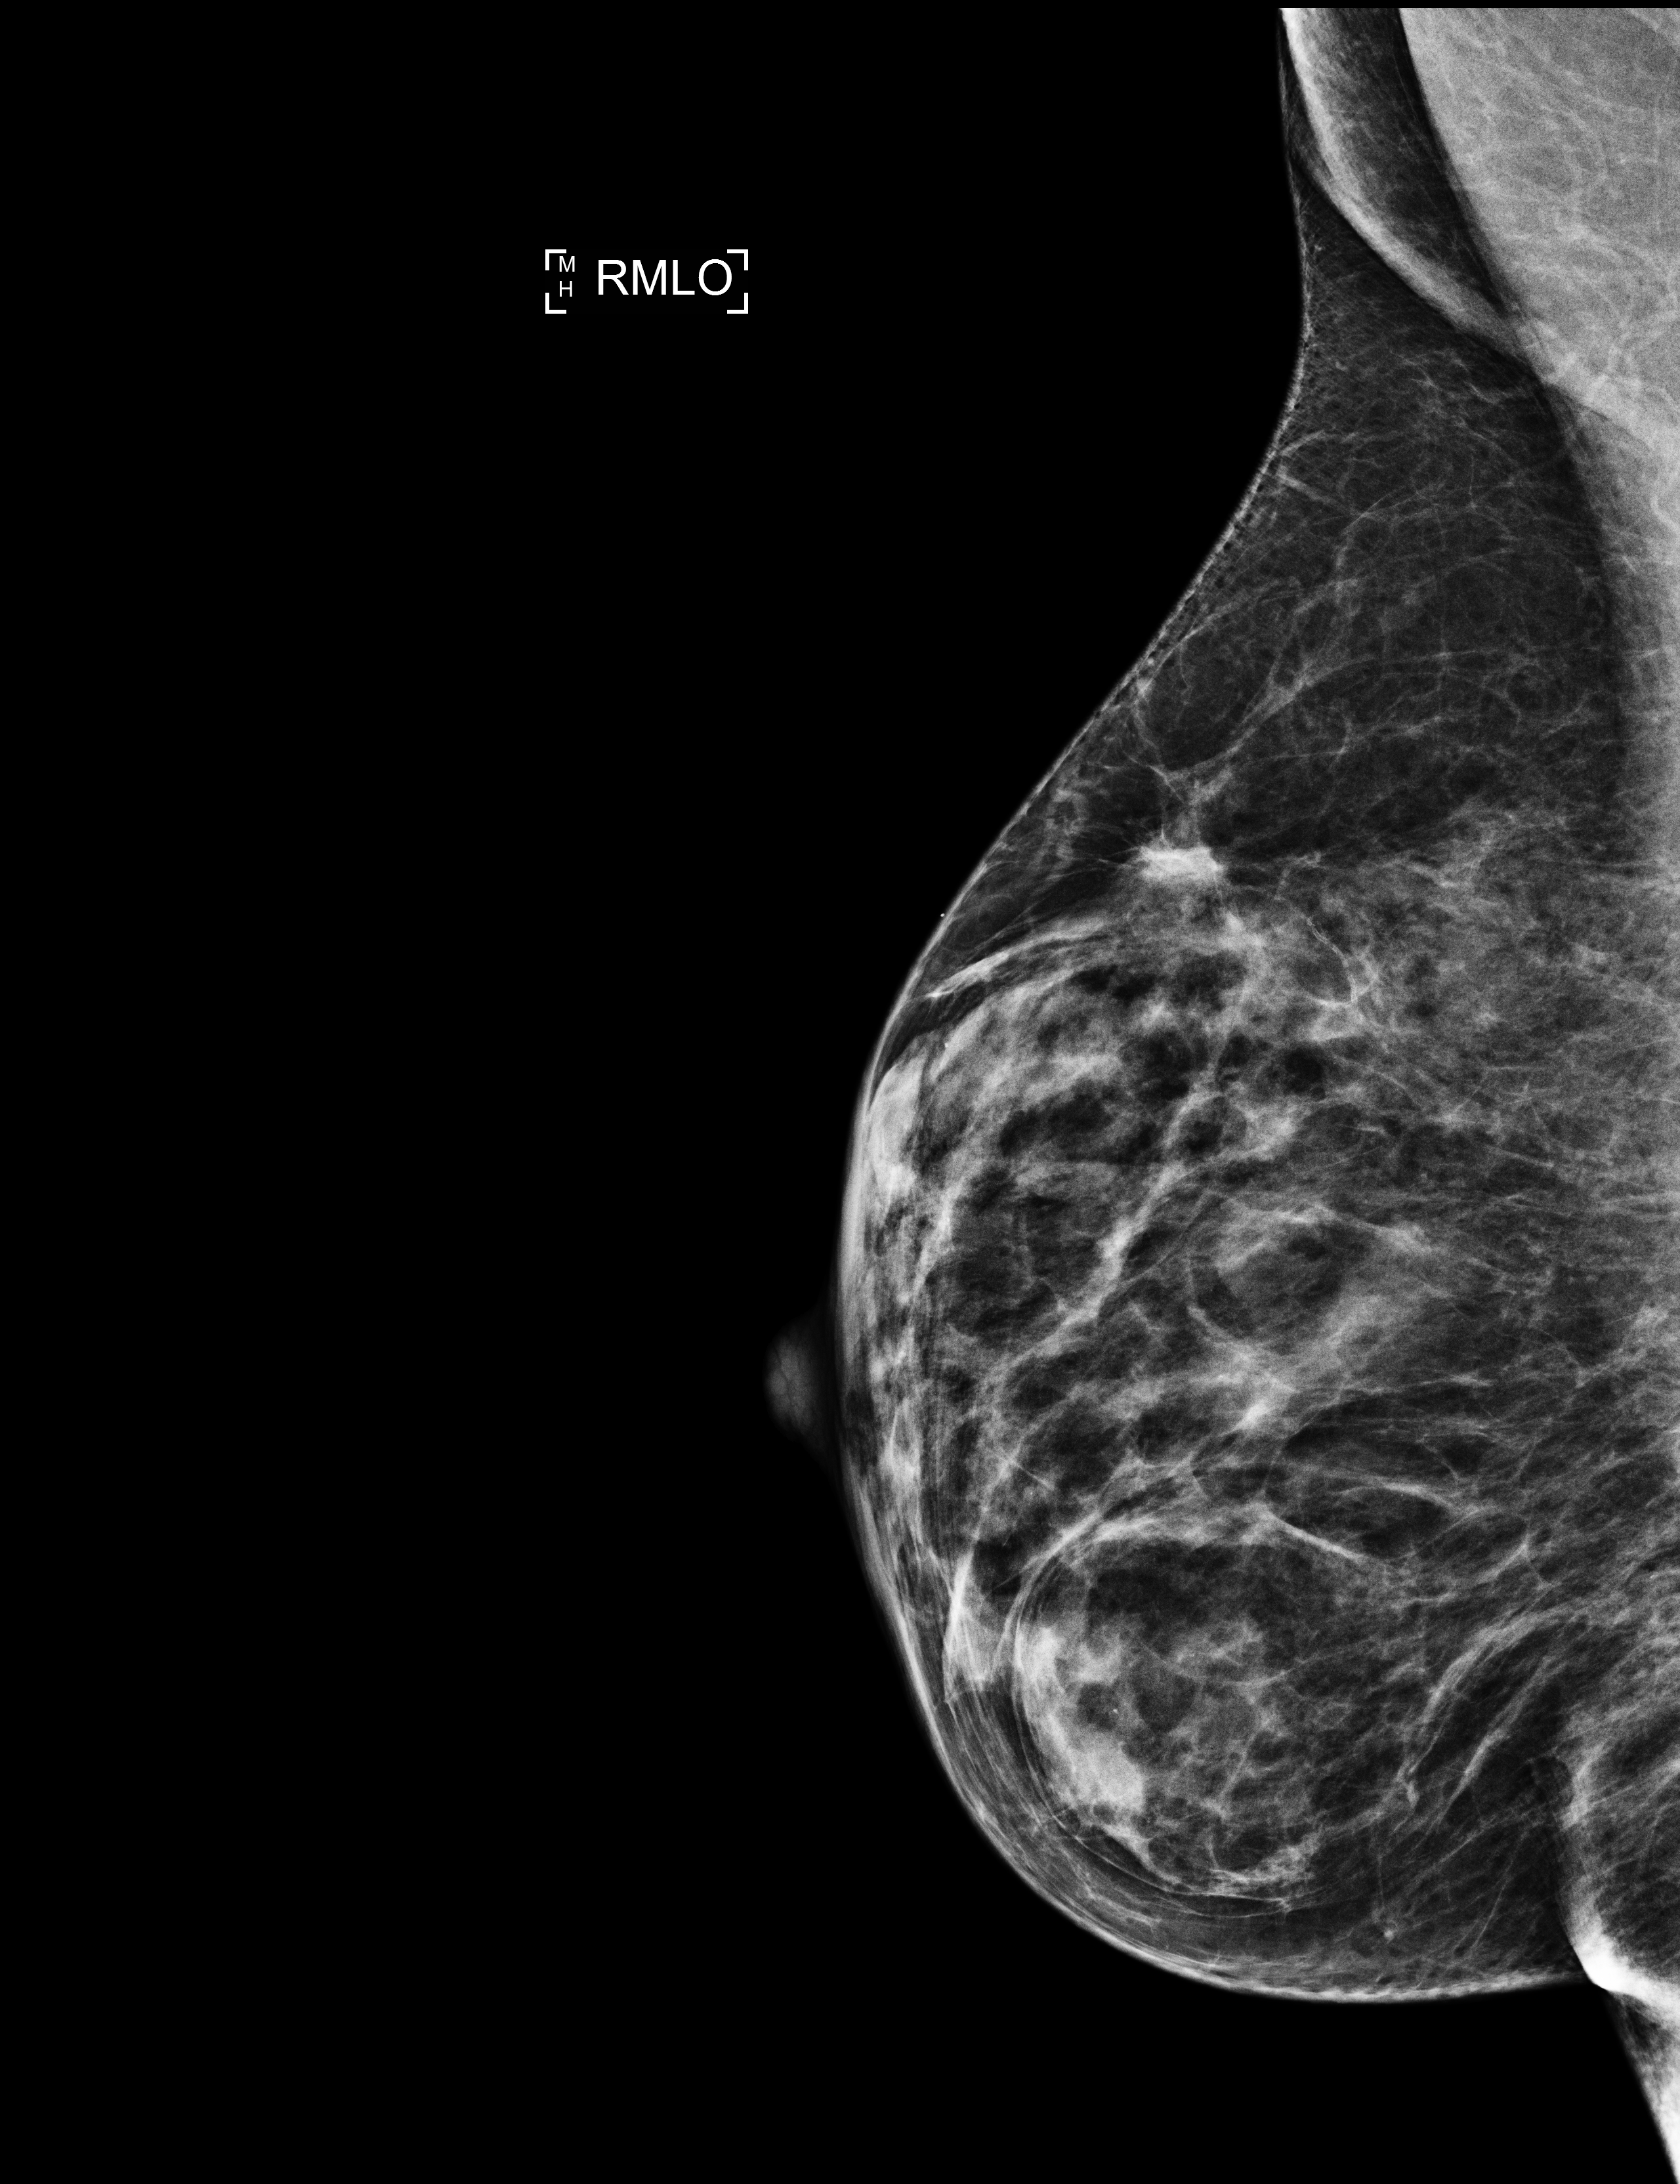
Screening examination.
Image type: full-field digital mammogram. Breast: right. Projection: mediolateral oblique (MLO) view.